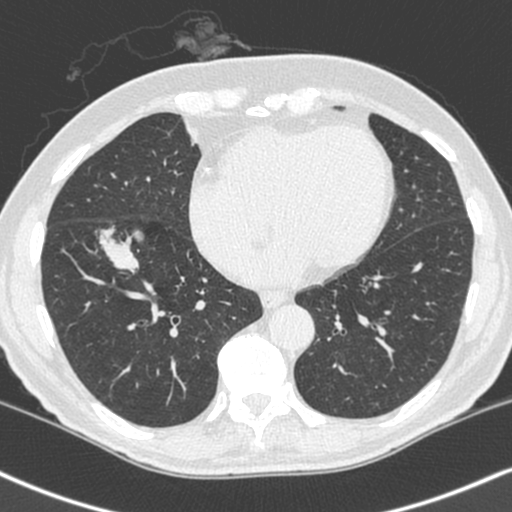
Chest CT (low-dose screening protocol), one axial image; first (baseline) screen; lung window (W 1500 / L -600 HU); 1.3 mm slice thickness; slice 149 of 248 in the series. Male participant, aged 68 years at enrolment.
- Expert-annotated lung lesion, box from (x=84, y=217) to (x=159, y=287) px.
- Reader record for this screening exam (exam-level; its link to the box is not recorded): non-calcified nodule or mass ≥4 mm, right lower lobe, 34 × 17 mm, smooth margins, soft tissue attenuation.
- Official screen result: positive, change unspecified: nodule(s) >= 4 mm or enlarging nodule(s), mass(es), or other non-specific abnormalities suspicious for lung cancer.
- Later outcome: lung cancer diagnosed 24 days after this screen — combined small cell carcinoma, right lower lobe, stage IIIA (AJCC 6th edition), 41 mm at pathology.